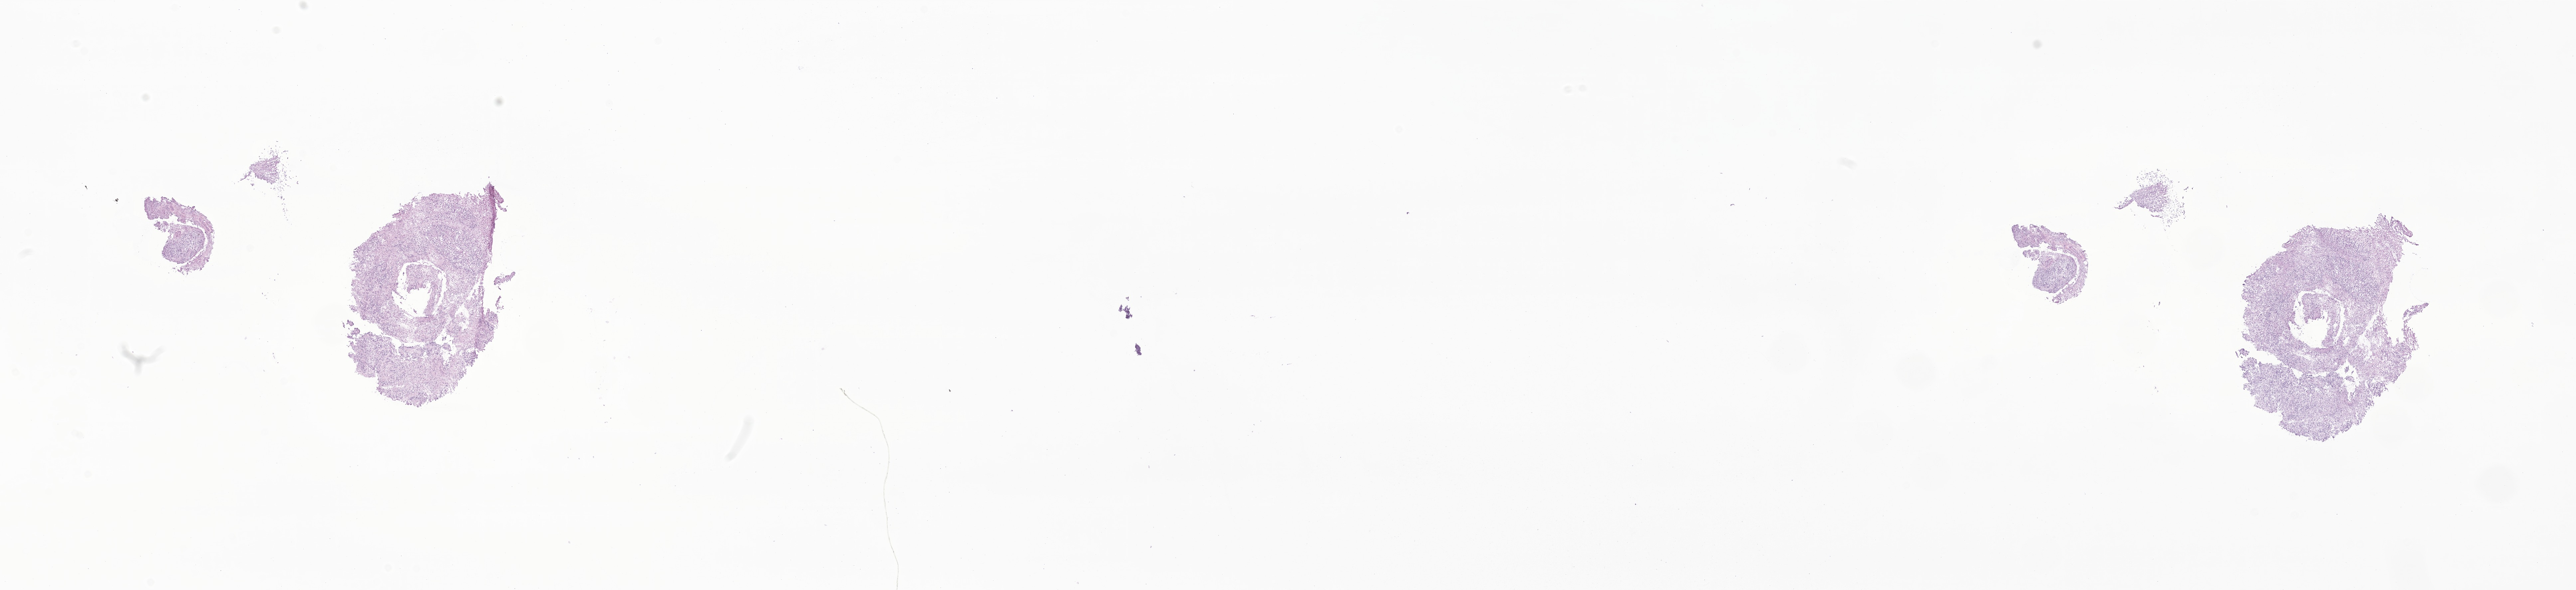
Digitized H&E-stained section of tumor tissue from the brain, shown as a low-resolution overview of the whole scanned area (about 32.7 x 7.5 mm); cryosection (OCT / tissue freezing medium). Female patient, age 35 months (2 years 11 months).
- recorded diagnosis: Ependymoma, NOS